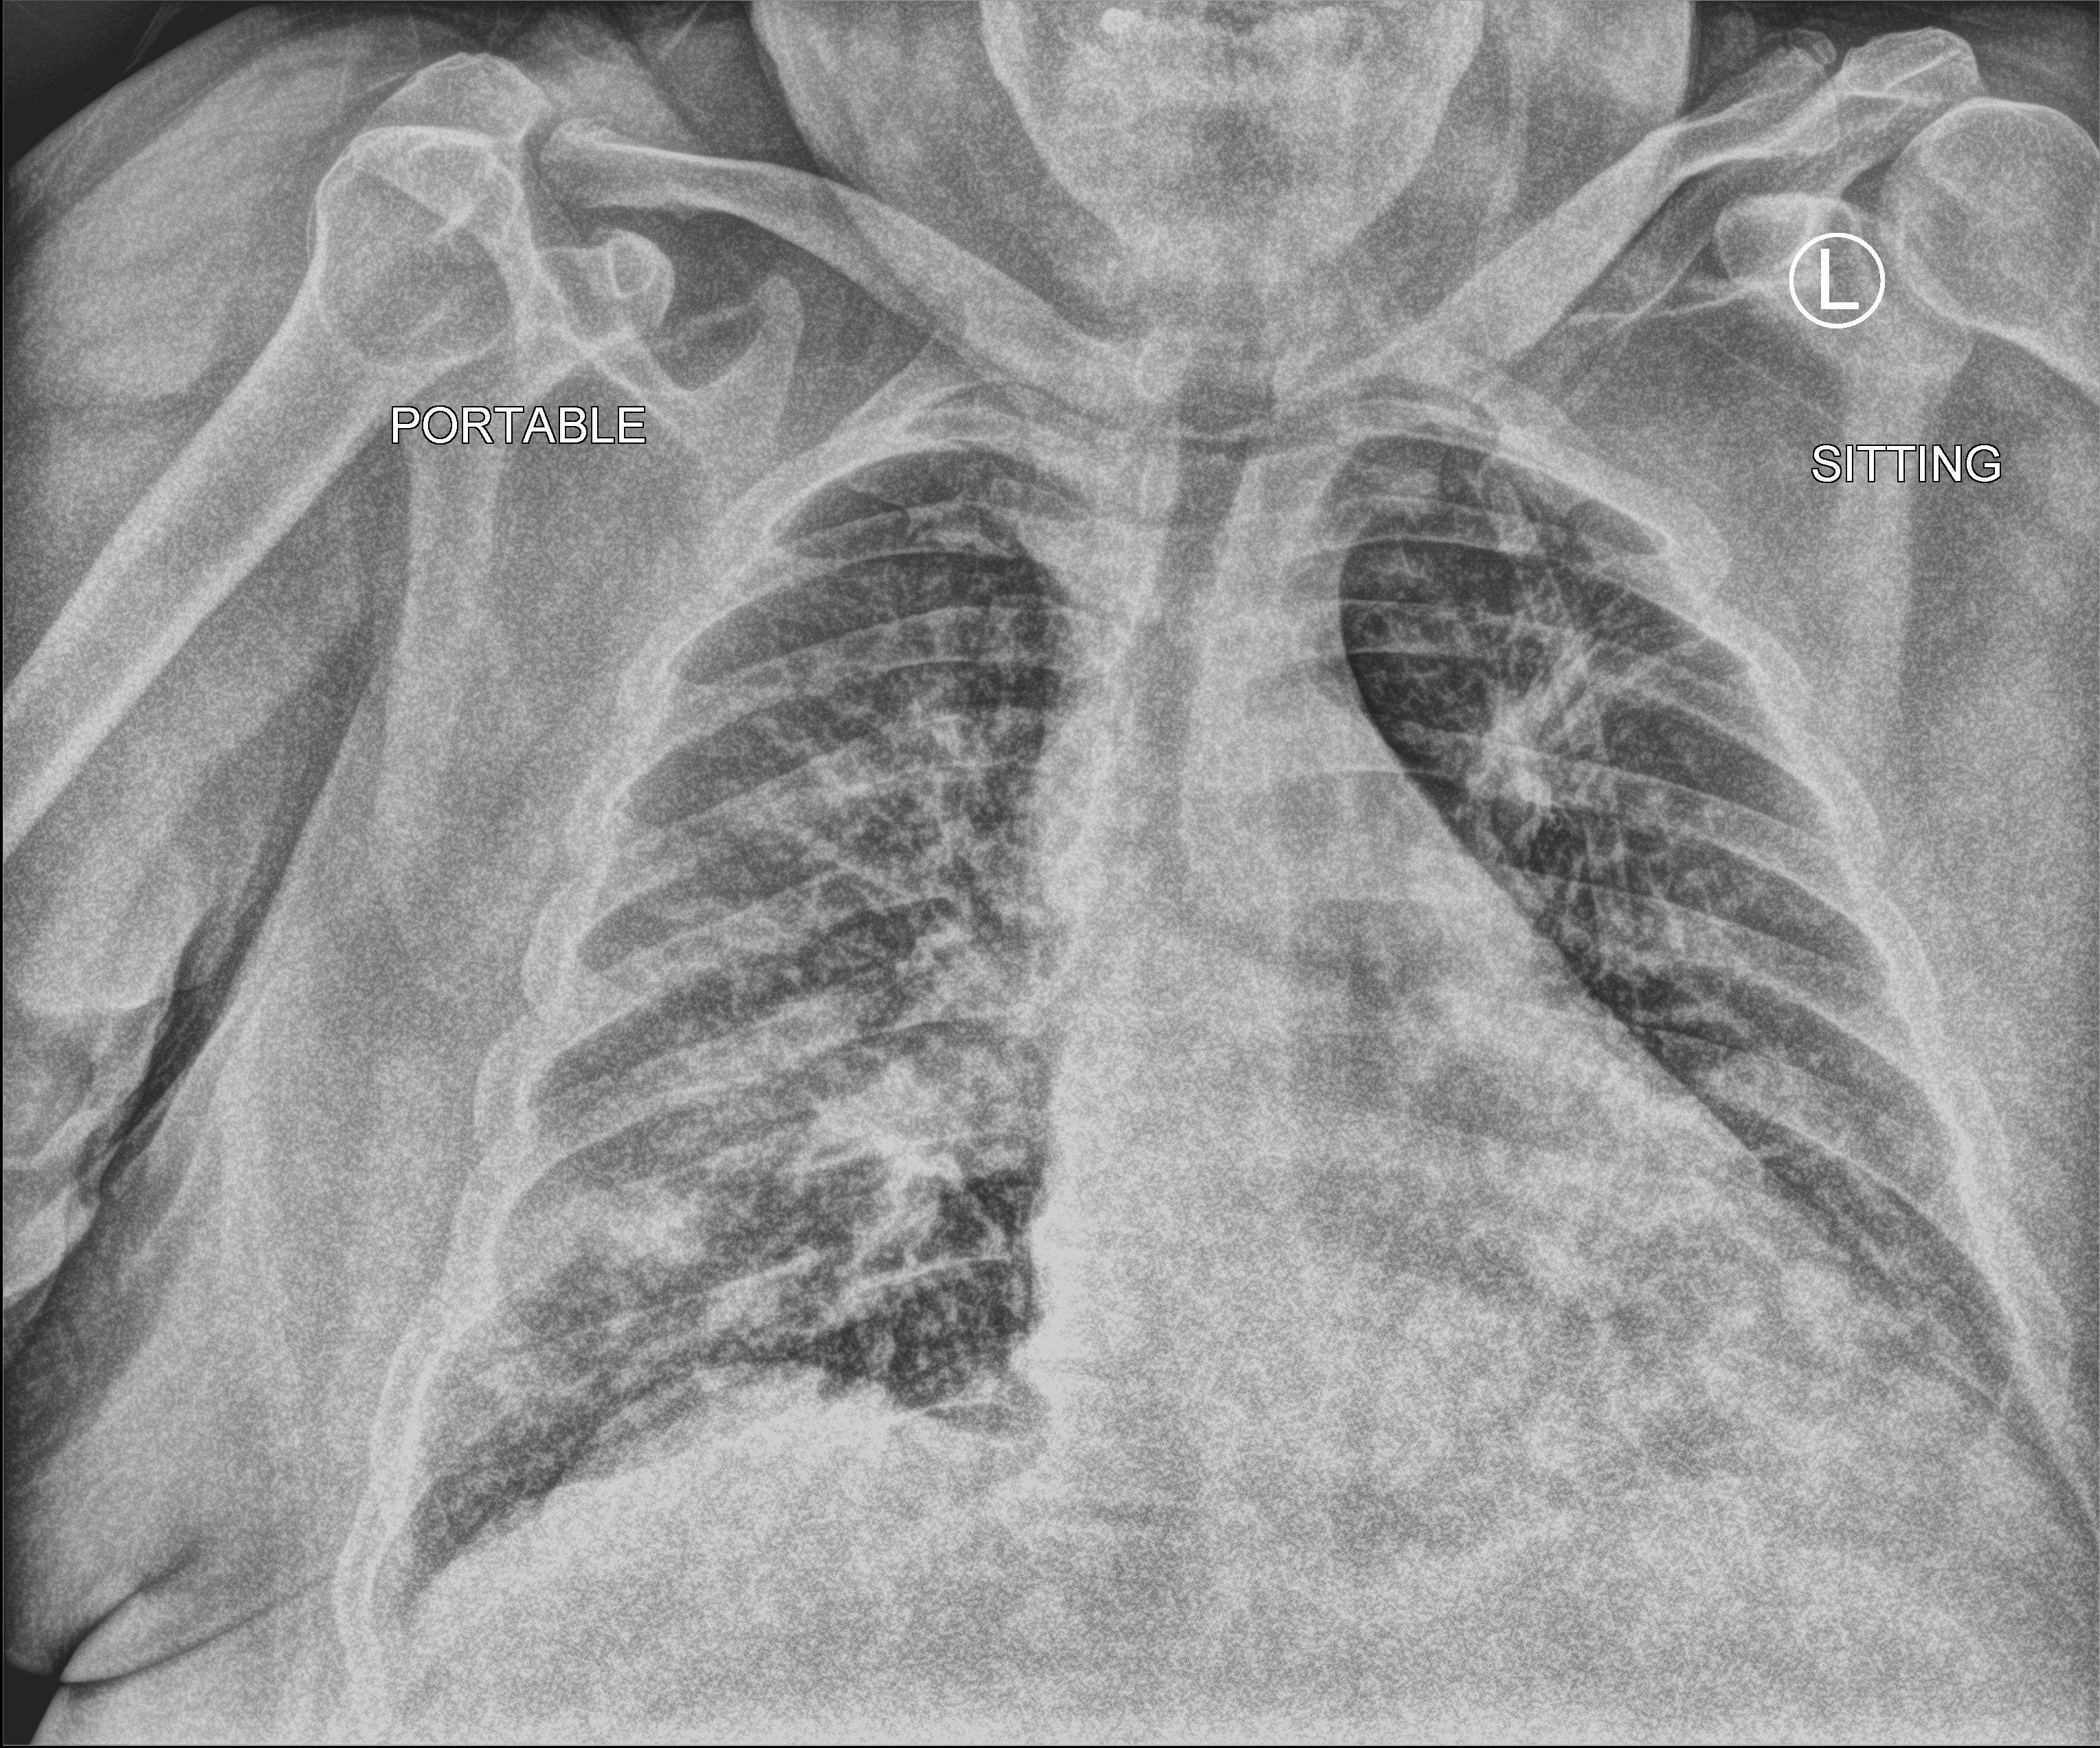
Chest X-ray (portable). Patient hospitalised with COVID-19; male, aged 60–74 years.
Admission-level facts for this patient (not findings on this image; timing relative to this image not recorded): COPD (admission record): no; admitted to intensive care during this hospital stay: yes; hypertension (admission record): no.